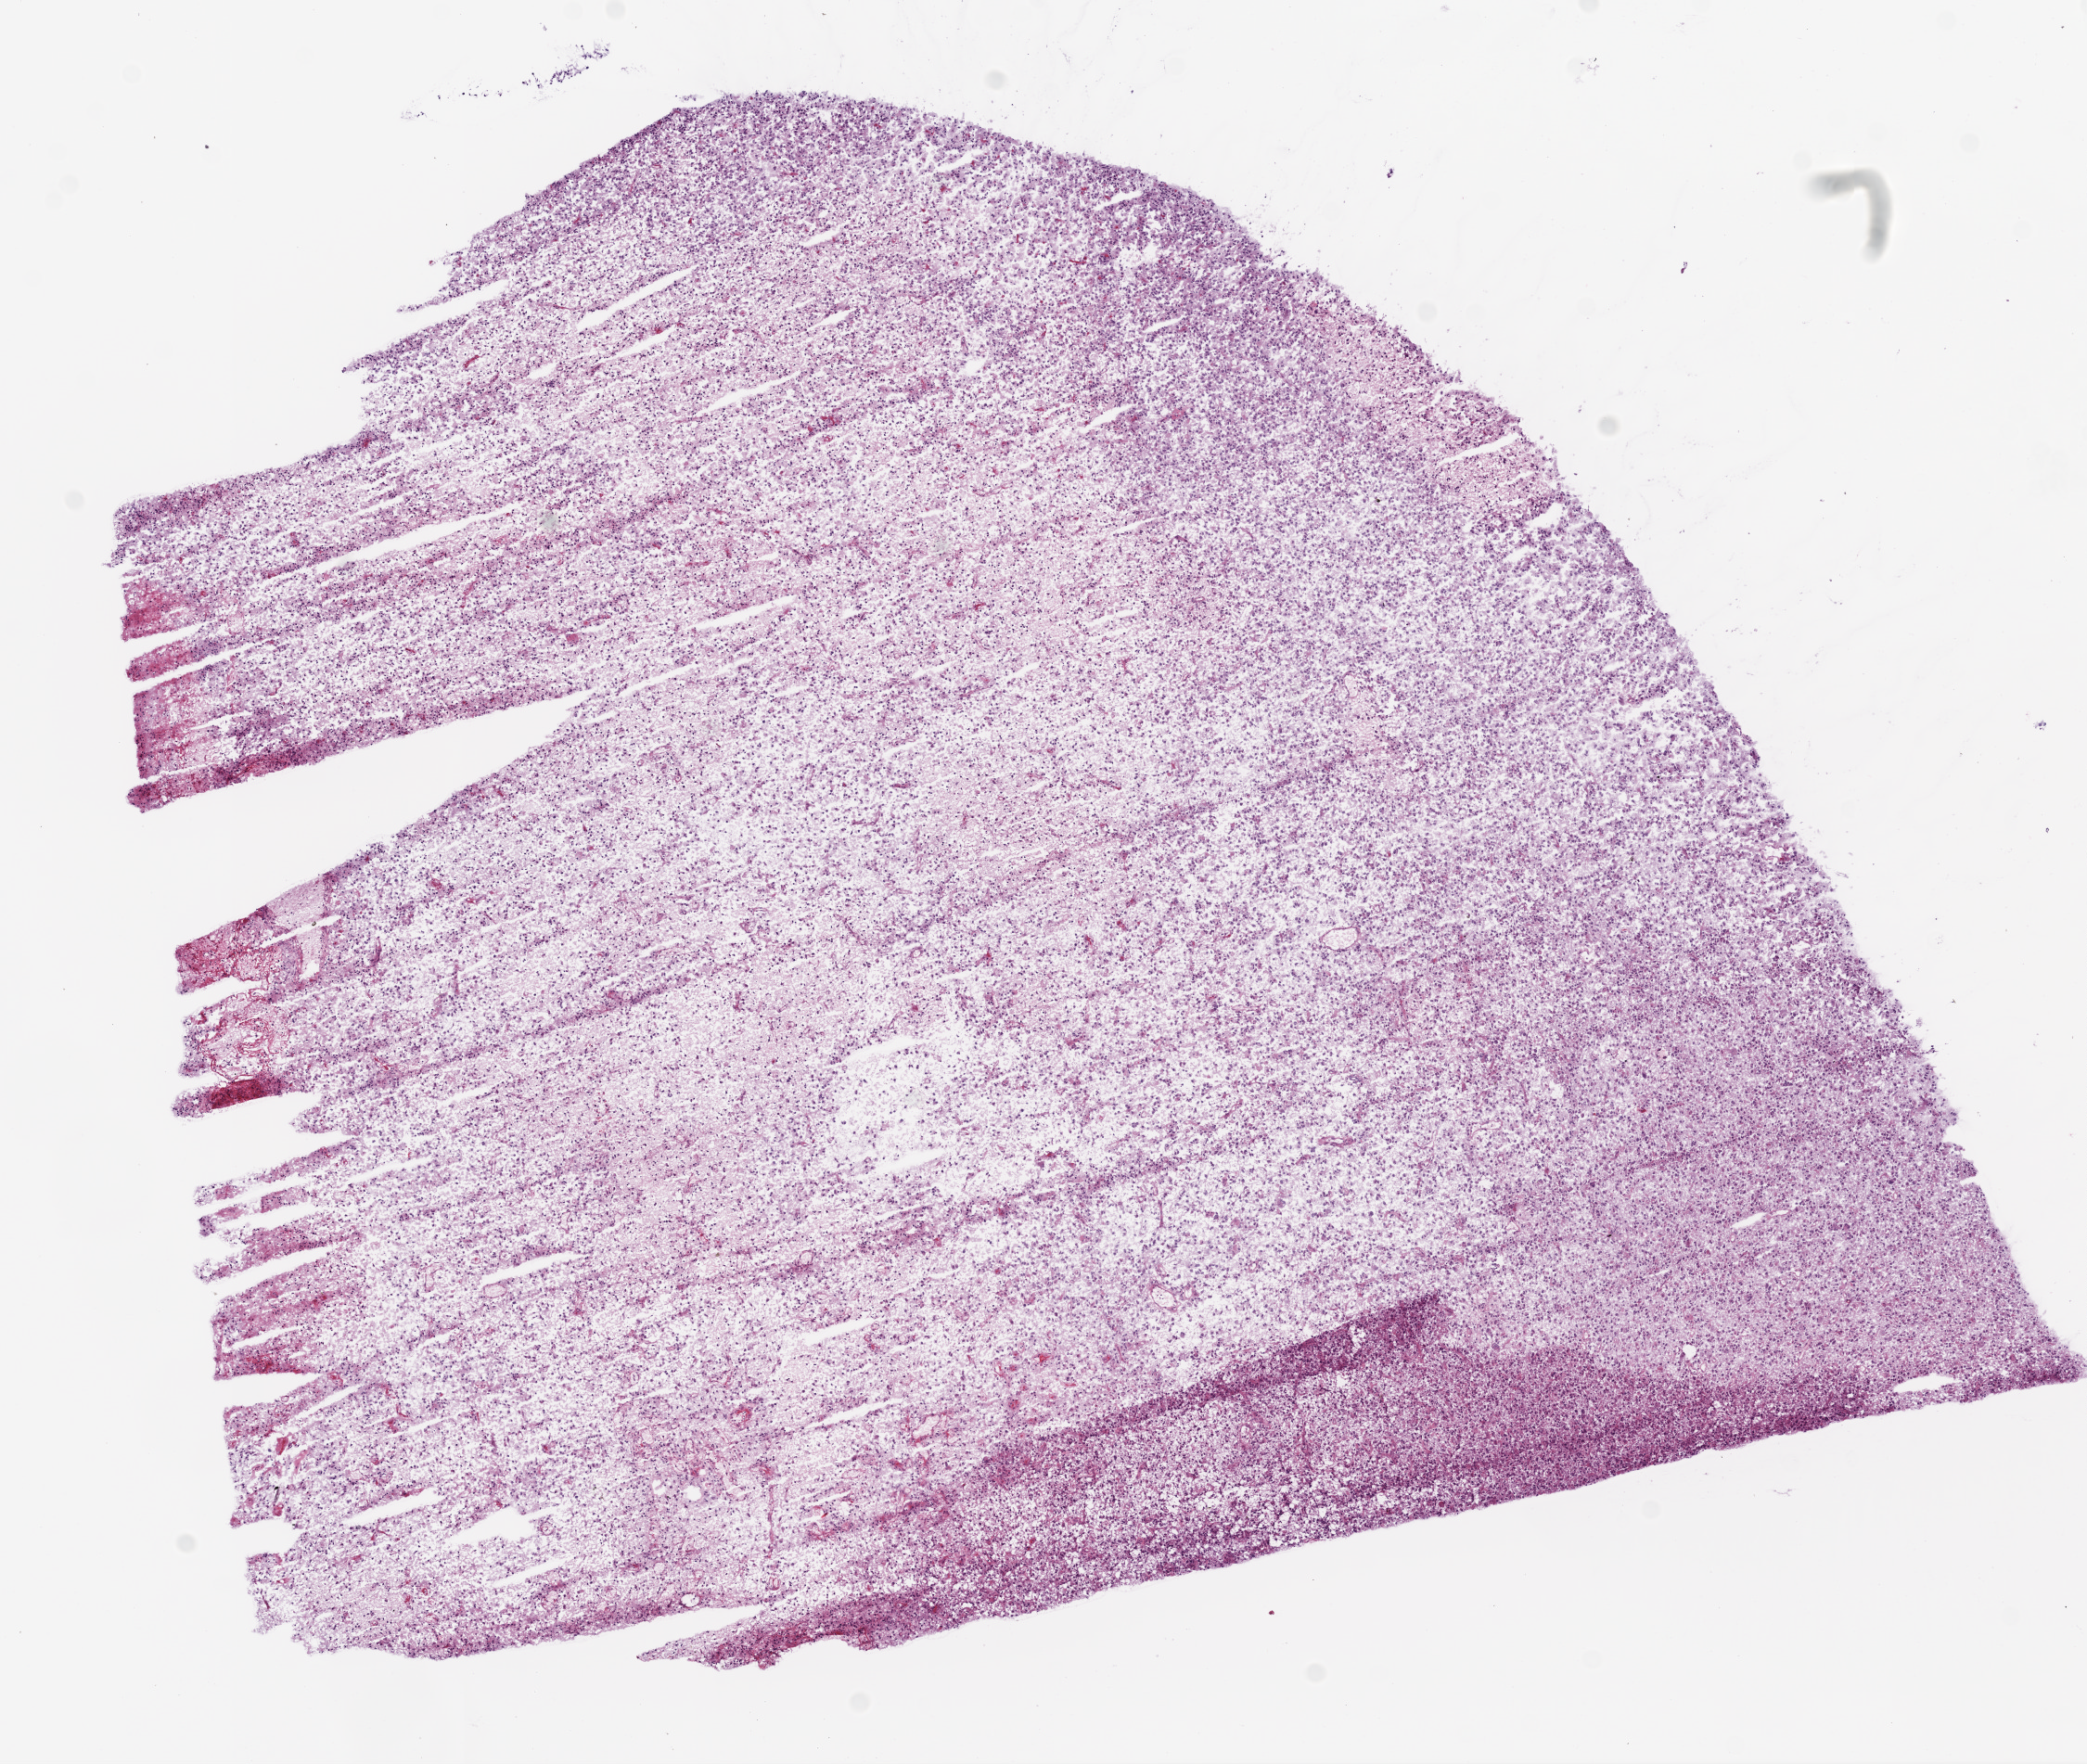
Whole-slide histology image, H&E, whole scanned area (about 9.0 x 7.6 mm, from a 20x scan) shown as a low-resolution overview. Frozen section. Sample: primary tumour, brain. Male, age 45 years at initial diagnosis. Slide review estimates, as recorded: tumour cells 93%, tumour nuclei 80%, normal cells 0%, stromal cells 0%, necrosis 7%.
Histologic diagnosis: Glioblastoma.